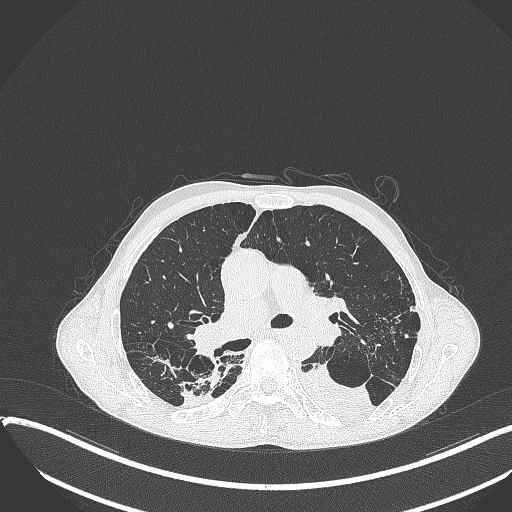
Chest CT, one axial slice; slice 235 of 401 in the series (ordered by position); lung window (W 1500 / L -600 HU); 1 mm slice thickness; 512 × 512 image matrix. Patient: male, 57 years. From the clinical record (not read from this slice): clinical TNM (as recorded): T4 N0 M0.
Annotated regions visible in this slice (bounding box drawn by a radiologist):
- lung tumour (recorded histology: squamous cell carcinoma): bounding box <301,364,374,423> (left, top, right, bottom; pixels)